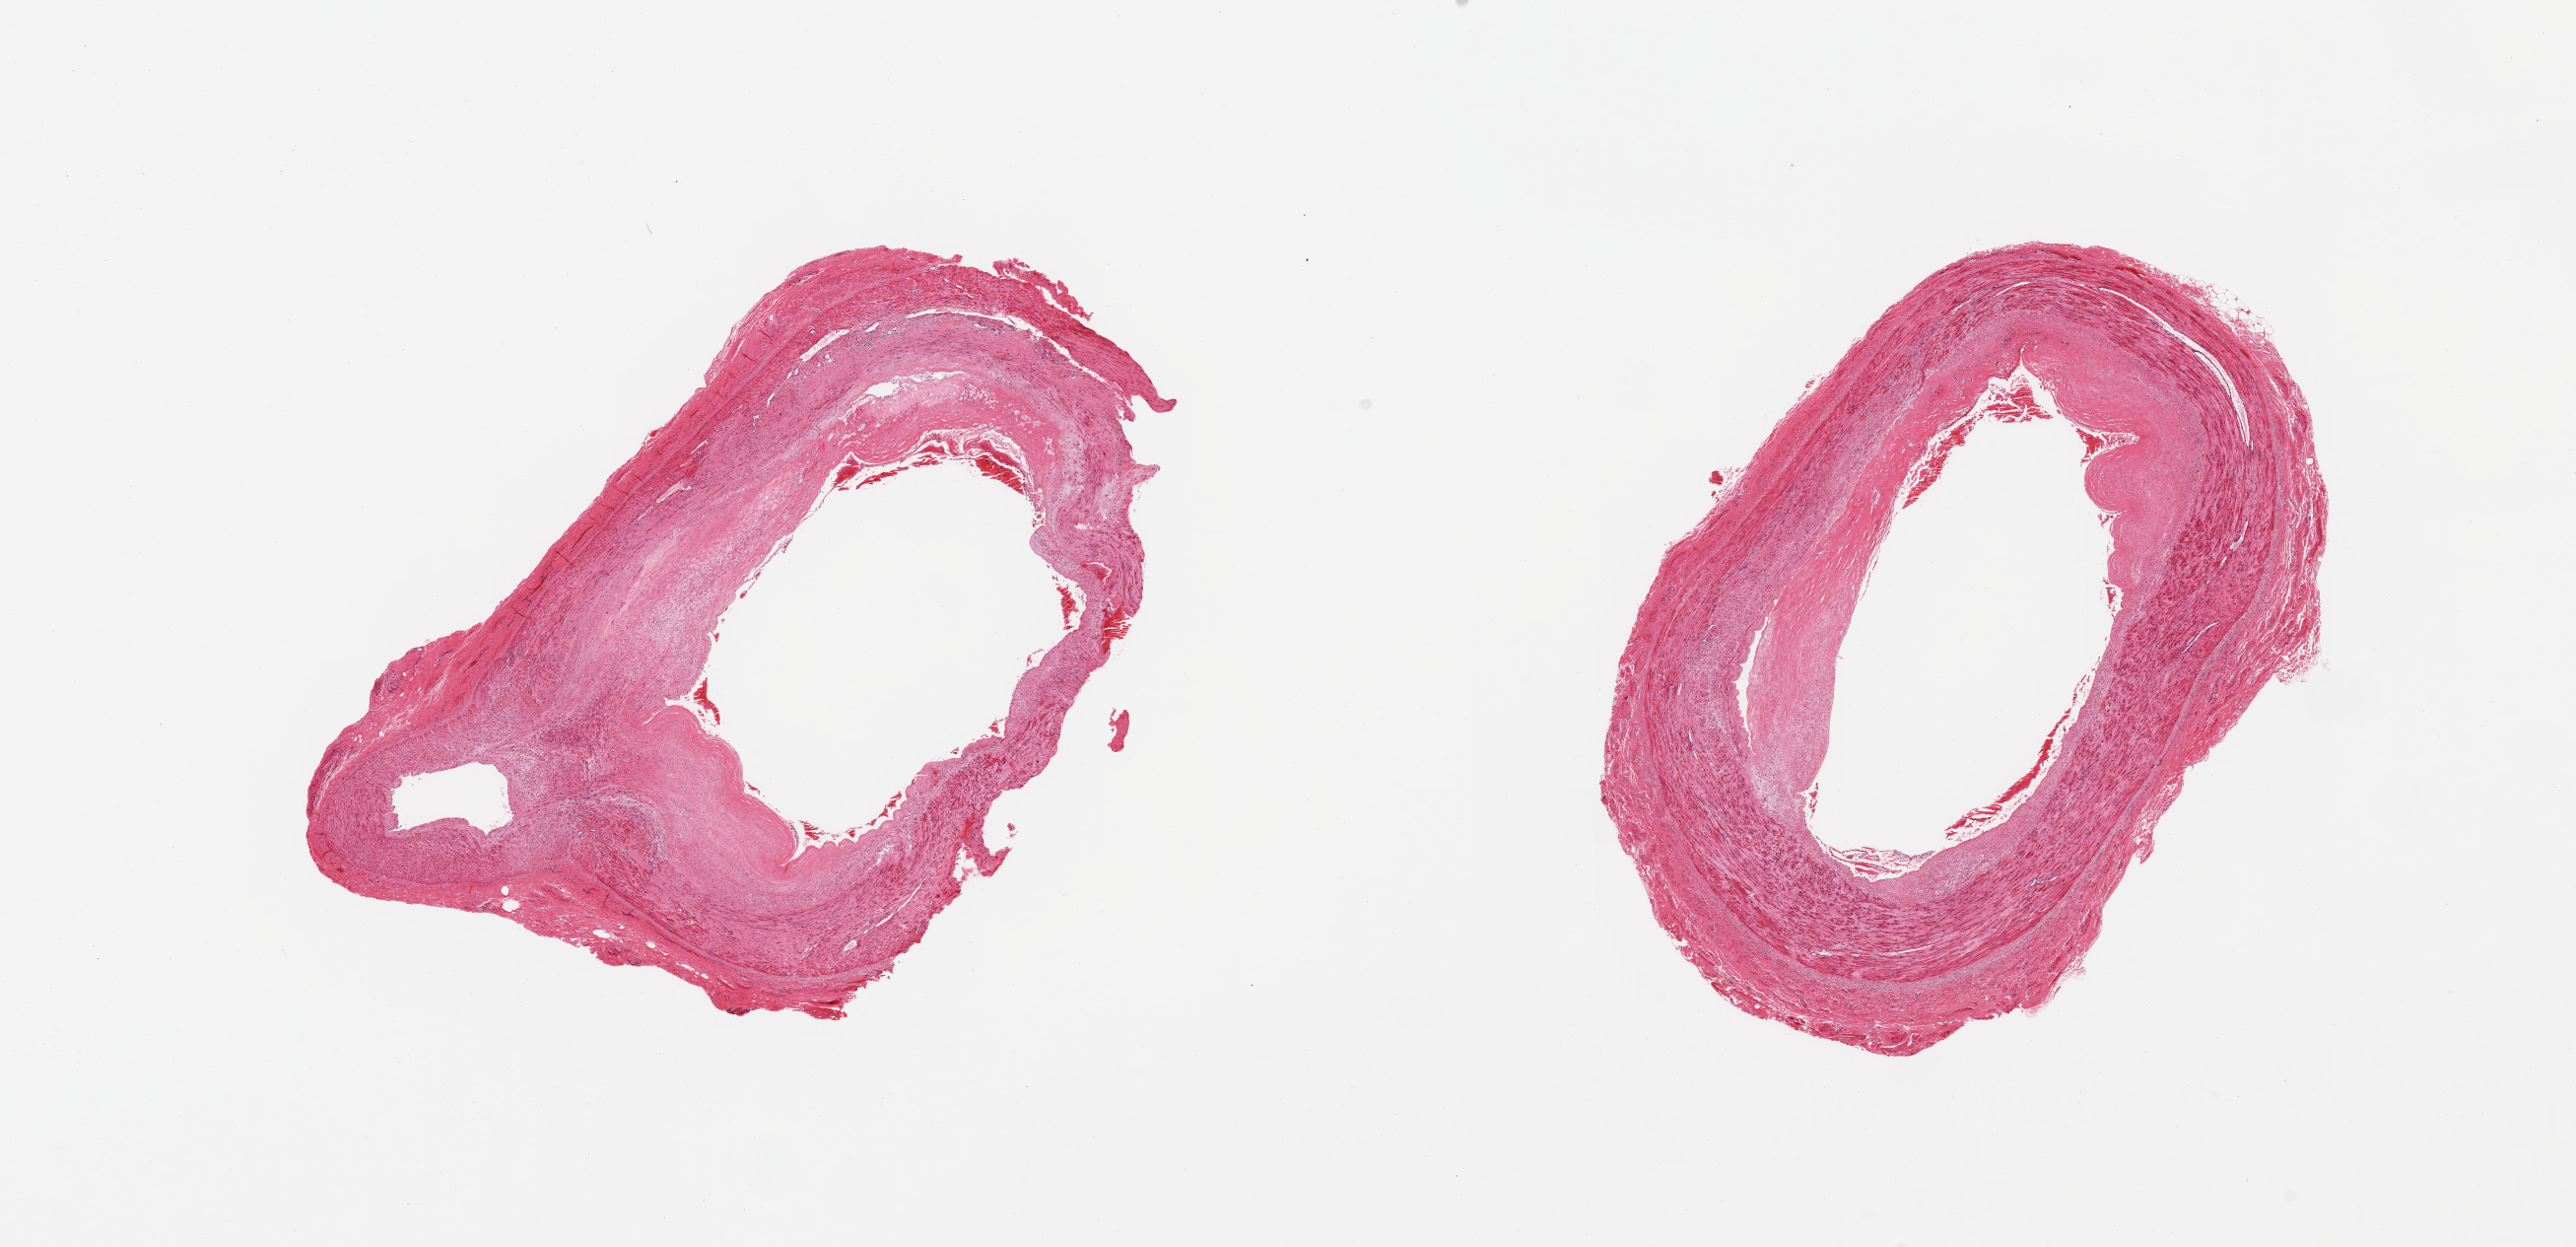
Whole-slide image, haematoxylin and eosin stain, shown as a low-resolution overview of the whole scanned area (about 20.7 x 10.0 mm). PAXgene-fixed, paraffin-embedded tissue. Sampled site (target tissue): tibial artery. Tissue donor sample. Donor: male.
- reviewer comment on this tissue sample: 2 pieces, ~50-60% occlusive atherosis; no adherent fat